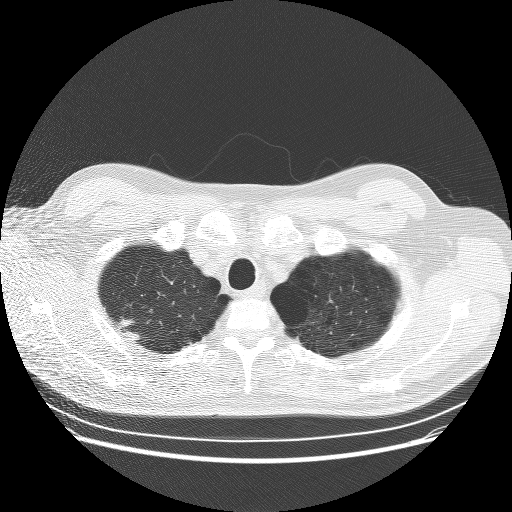
Low-dose screening chest CT, one axial slice. Position 232 of 253 along the scan axis. Reconstruction kernel BONE. 120 kVp. Lung window (W 1500 / L -600 HU). 512 × 512 image matrix, field of view 370 × 370 mm.
Annotated regions visible in this slice (outlined manually by an expert reader):
- lesion 1 (tumor, upper lobe of right lung): bounding box <121,319,140,340> (left, top, right, bottom; pixels)